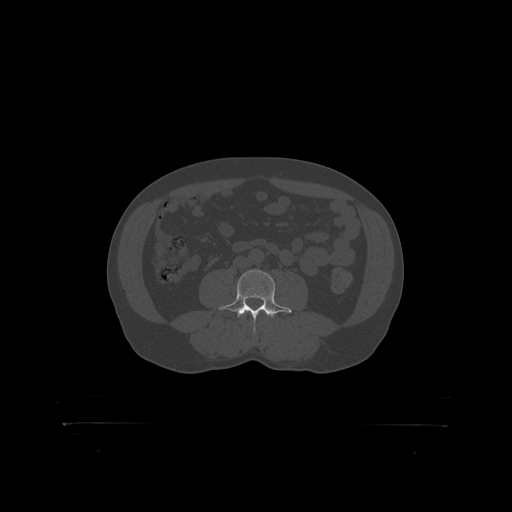
CT including the spine, one axial slice; slice 241 of 399 in the series (ordered by position); reconstruction kernel STANDARD; 120 kVp; bone window (W 1800 / L 400 HU); 512 × 512 image matrix. Patient: male, 46 years. From the clinical record (not read from this slice): primary cancer: skin.
Outlined on this slice (semi-automatically segmented with operator editing):
- L4 vertebra: bounding box <221,270,290,319> (left, top, right, bottom; pixels)